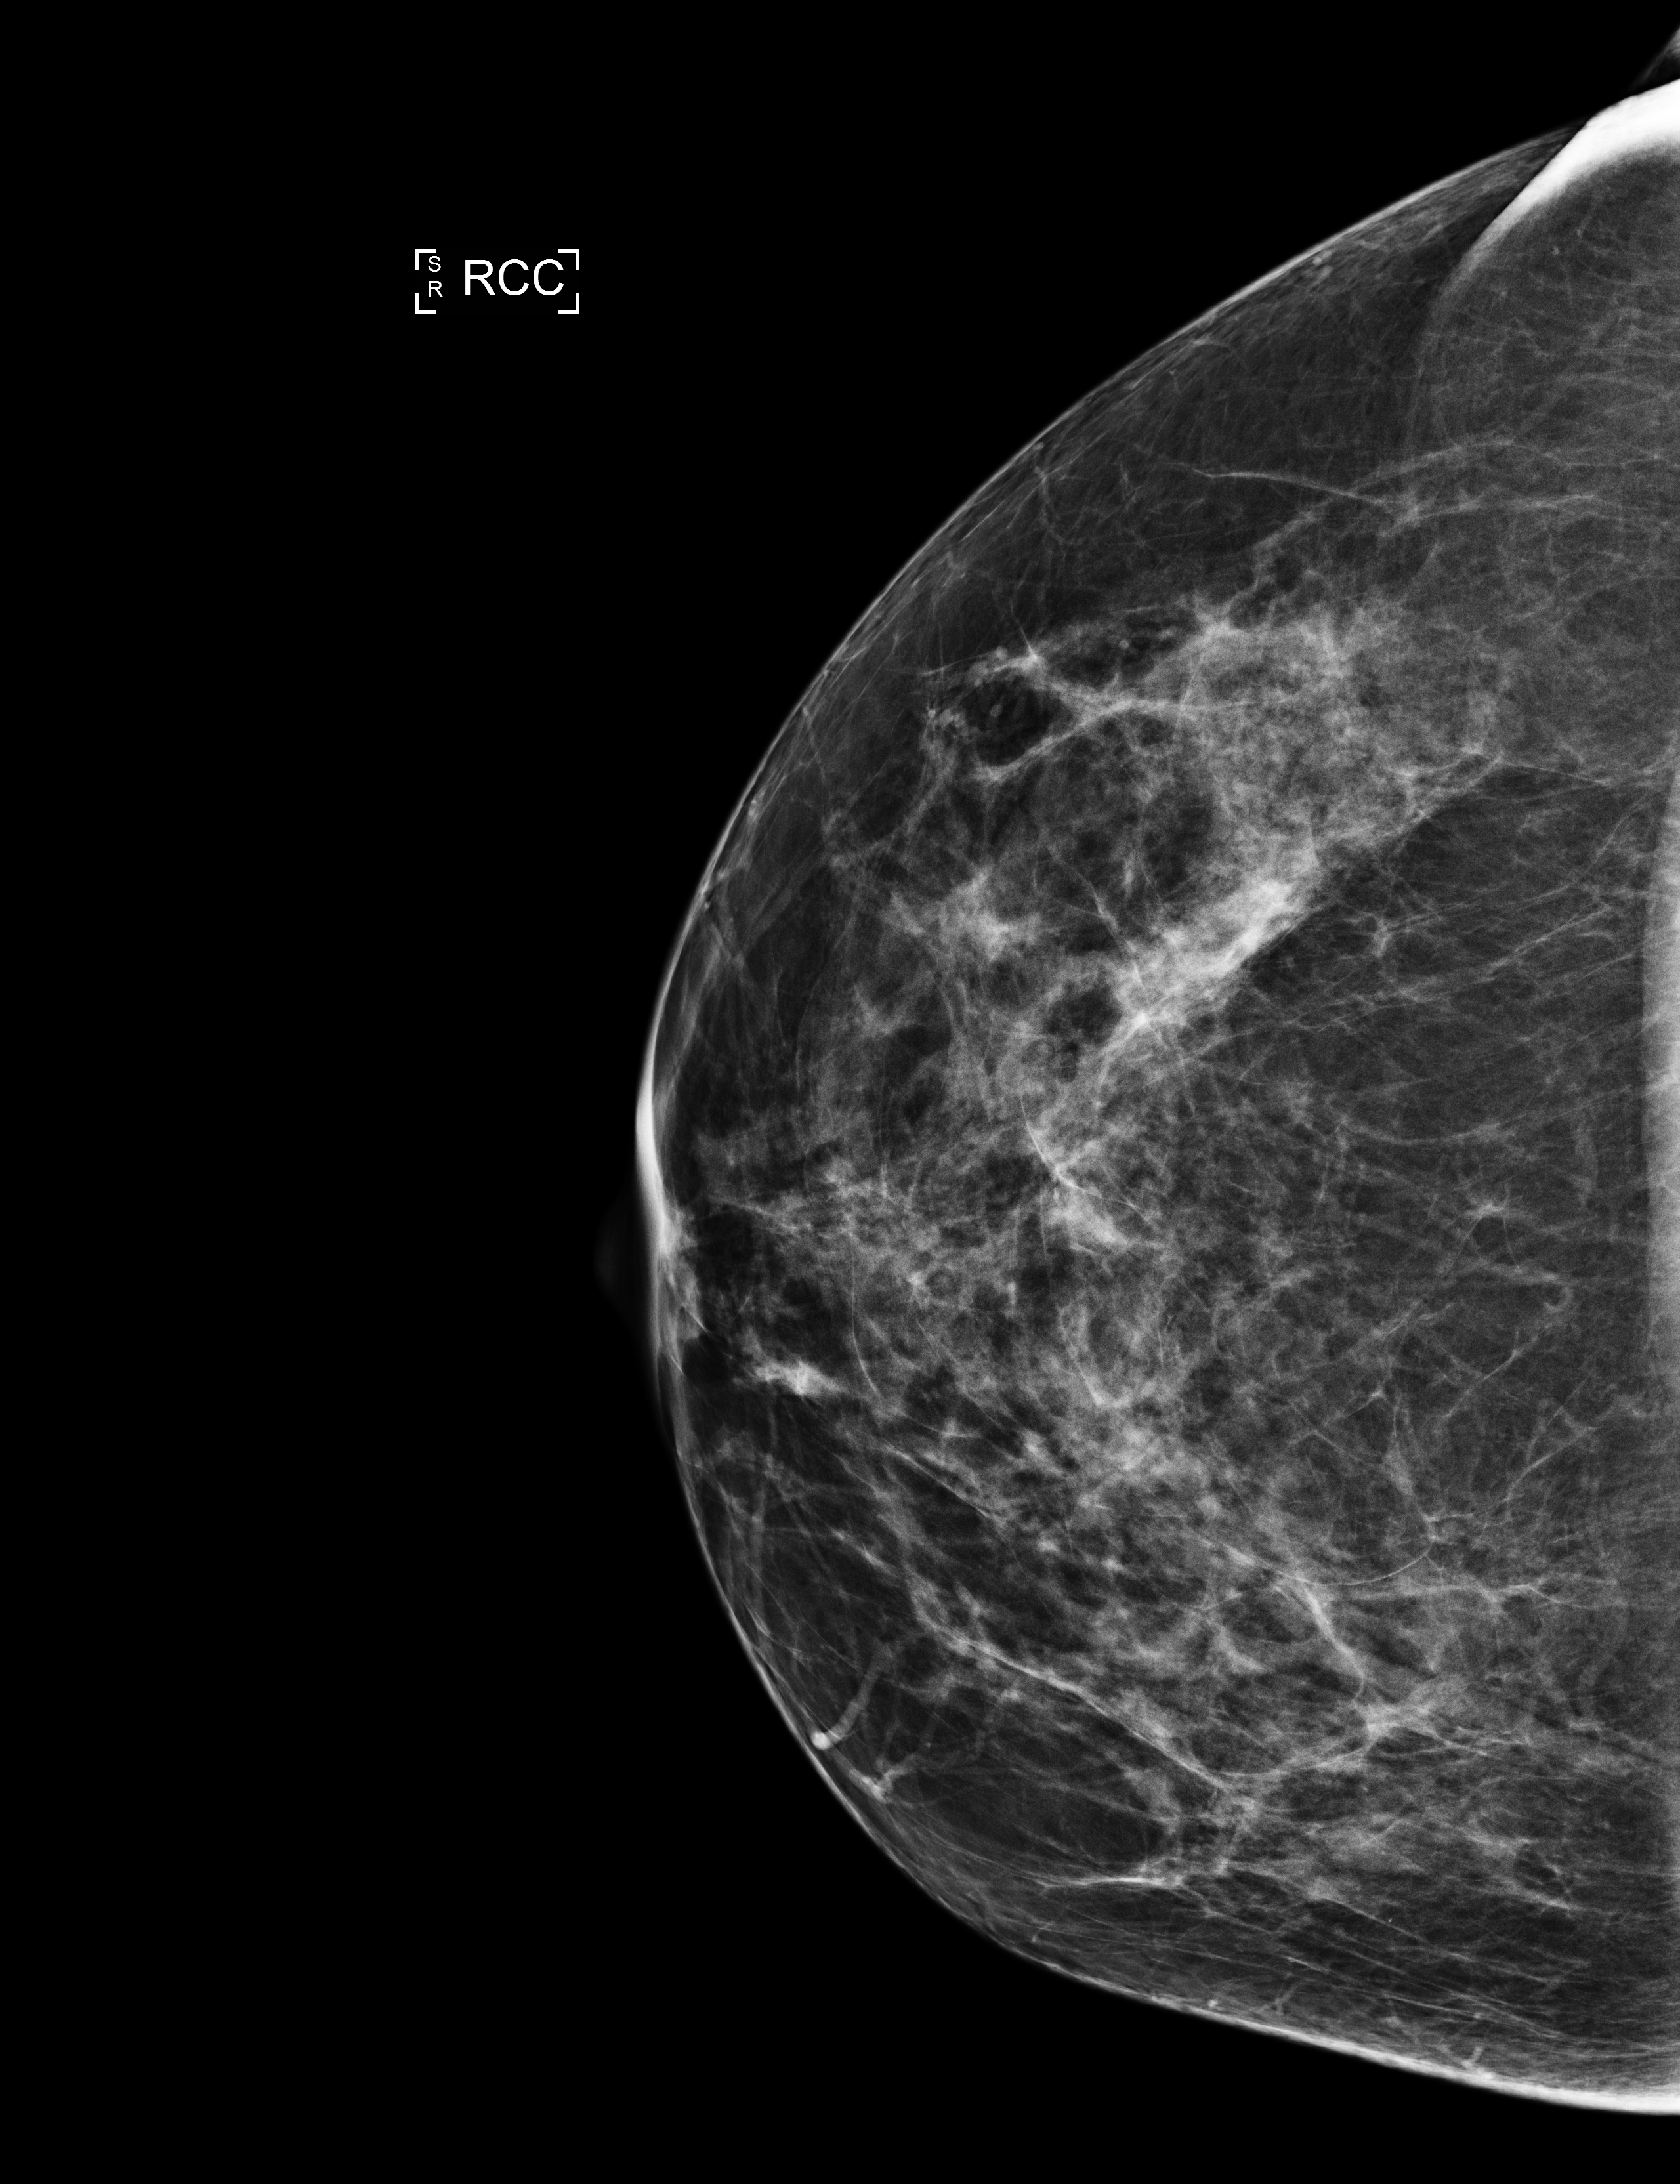
Digital mammogram (FFDM); right breast; craniocaudal (CC) view; screening examination; system: Selenia Dimensions. Female patient, age 50 years.
Breast density at the screening exam (both breasts): heterogeneously dense (BI-RADS density category c). Final BI-RADS assessment for this screening round (tomosynthesis exam, both breasts): category 1. Recall: no recall after this screen.